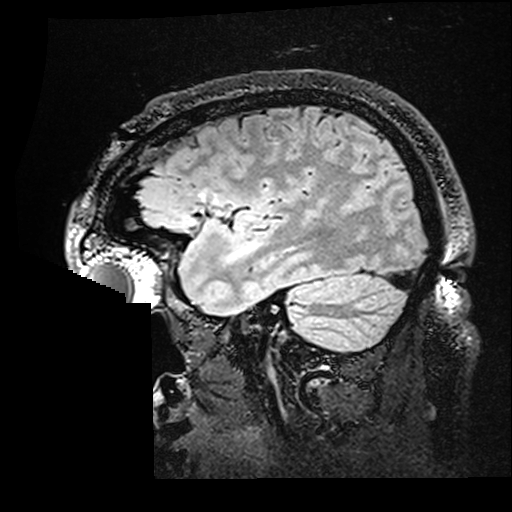
Brain MRI from a brain-tumour surgery series, one sagittal slice; slice 128 of 176 in the series (ordered by position); T2 FLAIR; 1 mm slice thickness; 512 × 512 image matrix, field of view 250 × 250 mm. From the clinical record (not read from this slice): histopathology: Astrocytoma; WHO grade: 2; IDH mutation: yes.
Outlined on this slice (expert manual segmentation):
- residual tumour: bounding box (x1, y1, x2, y2) in pixels: (239, 237, 256, 256)